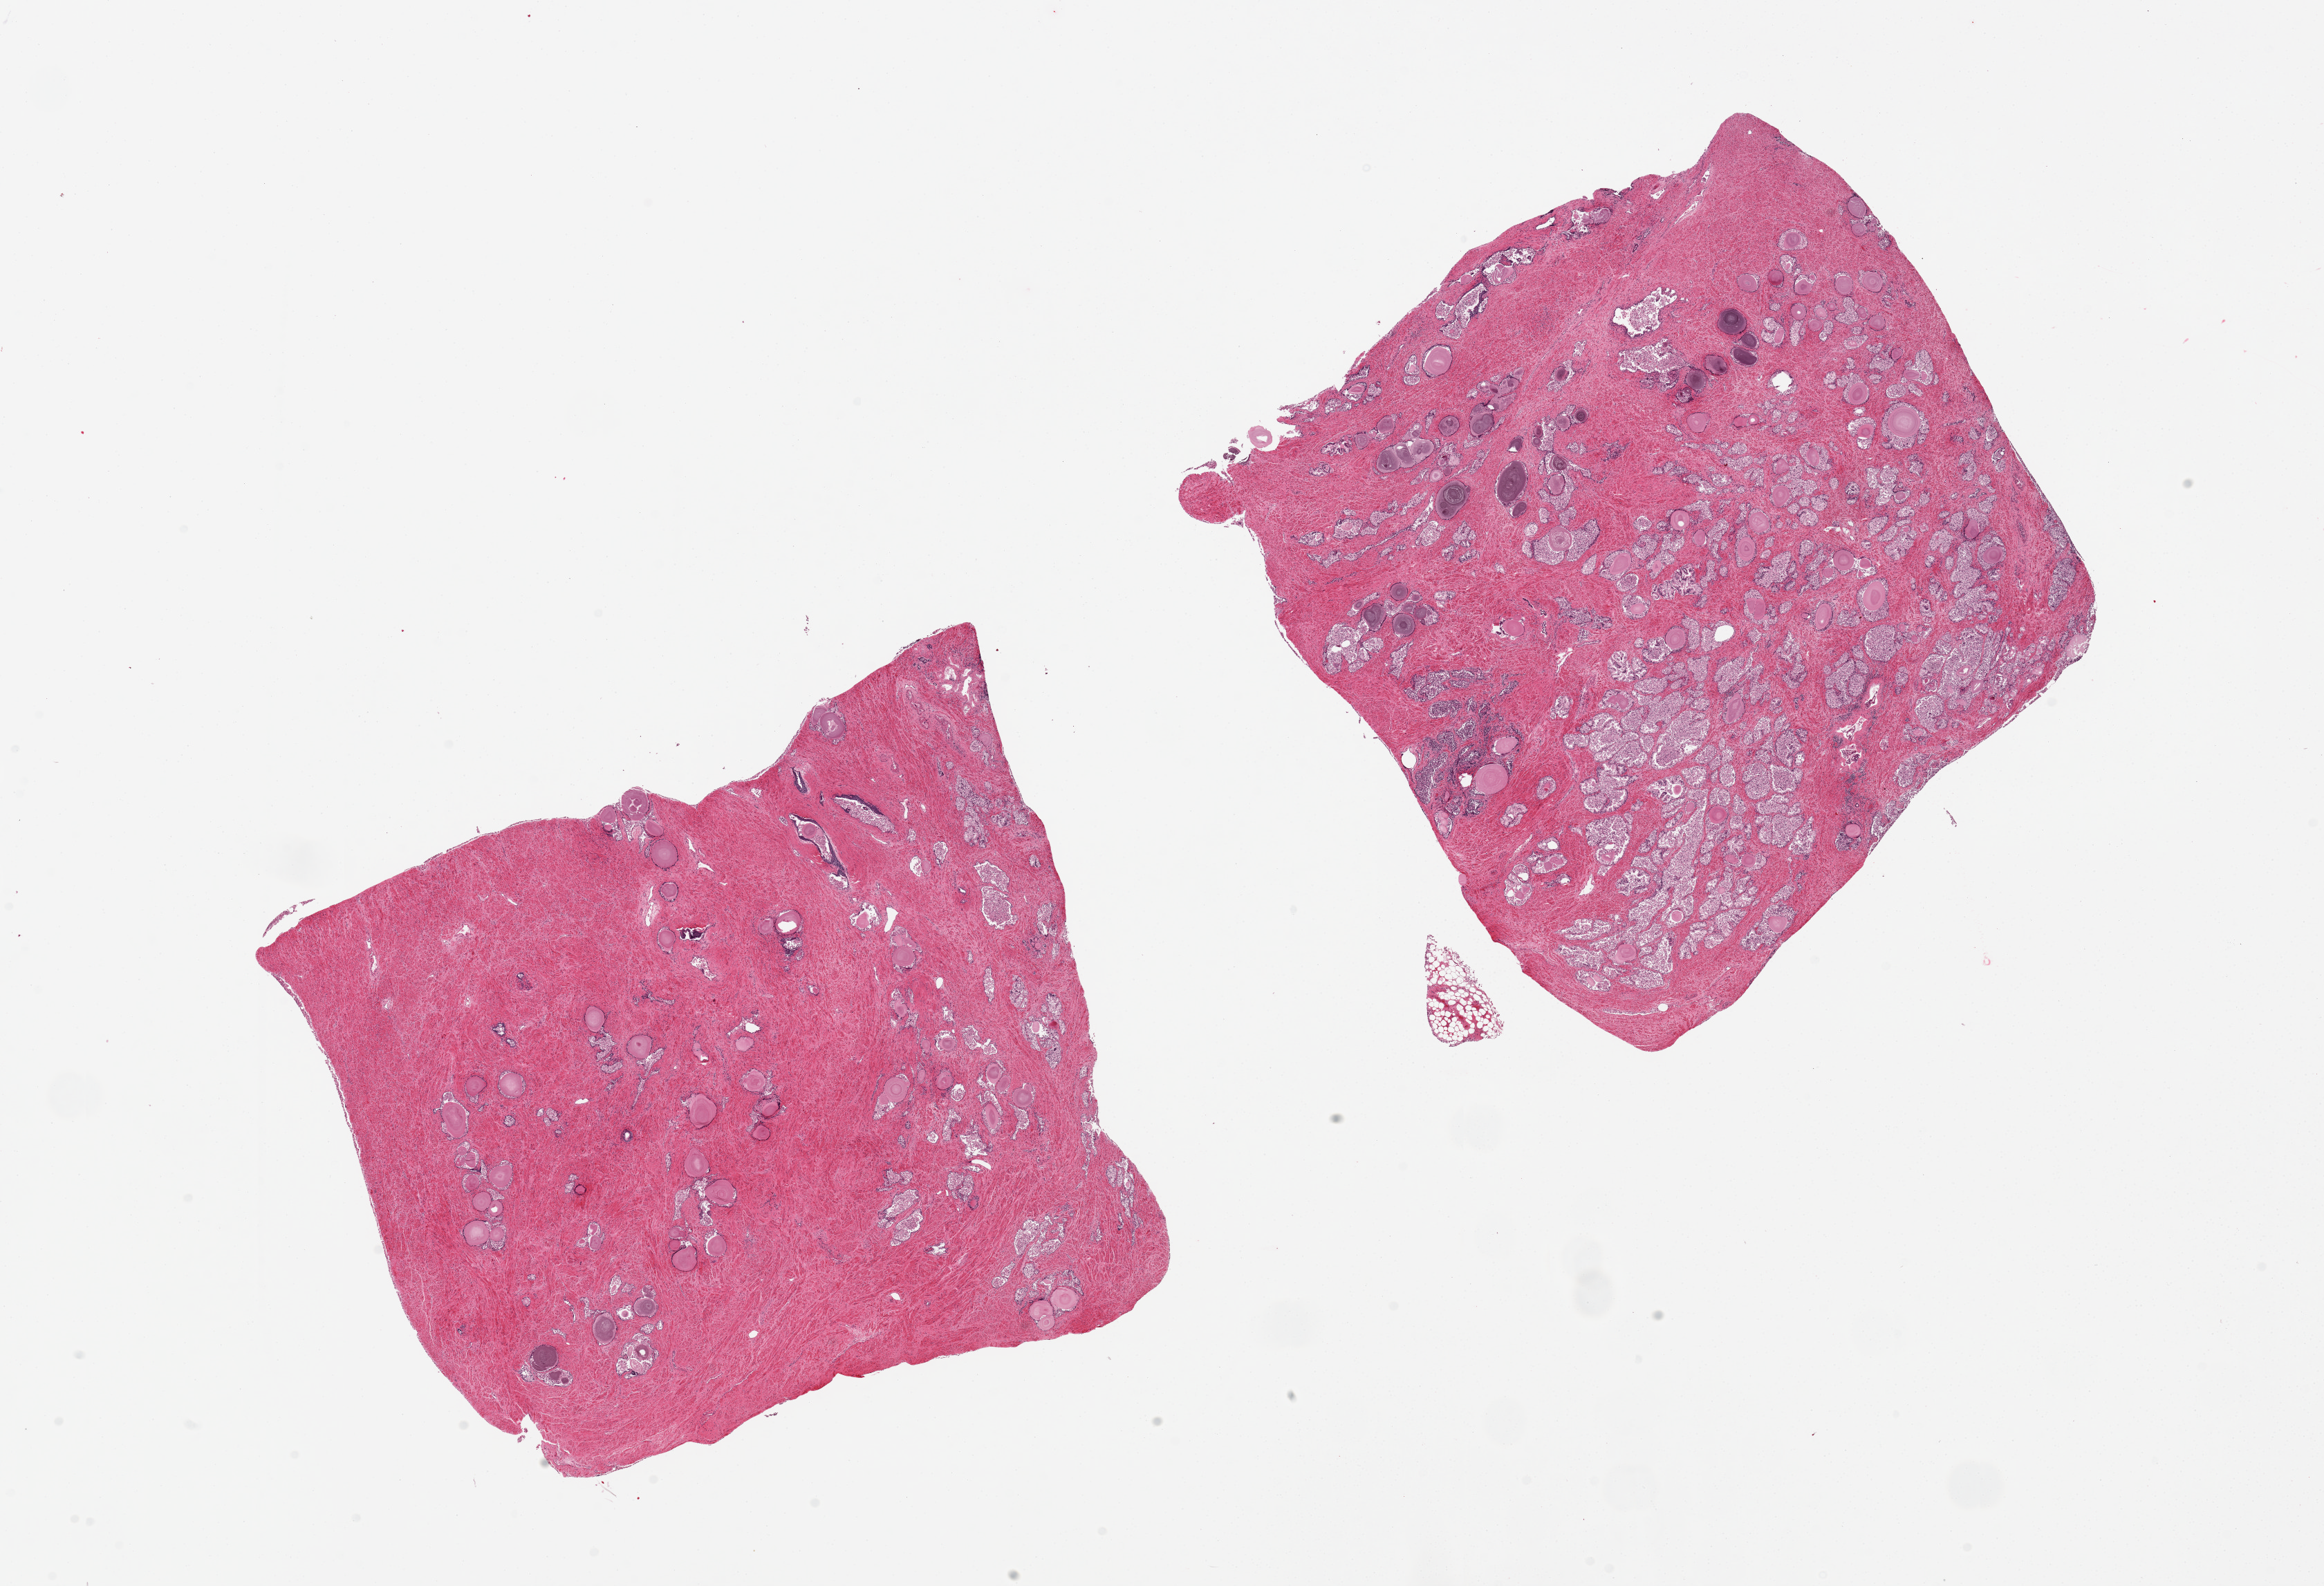
H&E whole-slide image, brightfield — shown as a low-resolution overview of the whole scanned area (about 26.6 x 18.1 mm, slide scanned at 20x). PAXgene-fixed paraffin-embedded (PFPE) section. Sampled site (target tissue): prostate. Tissue donor sample. Male donor.
- reviewer comment on this tissue sample: 2 pieces, glandular elements badly autolyzed